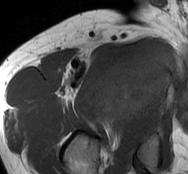
MRI of an extremity soft-tissue mass, one axial slice; slice 66 of 93 in the series (ordered by position); MR volume resampled by the dataset authors to the PET/CT grid (not the native acquisition matrix); 188 × 174 image matrix, field of view 184 × 170 mm. Male patient. From the clinical record (not read from this slice): histological type: undifferentiated - pleiomorphic; grade: high; site of the primary tumour: right thigh.
Outlined on this slice (expert contour drawn on MRI and transferred to this co-registered scan by the dataset authors):
- gross tumour volume including surrounding oedema: bounding box <95,42,178,127> (left, top, right, bottom; pixels)
- gross tumour volume (mass): <95,46,176,125>